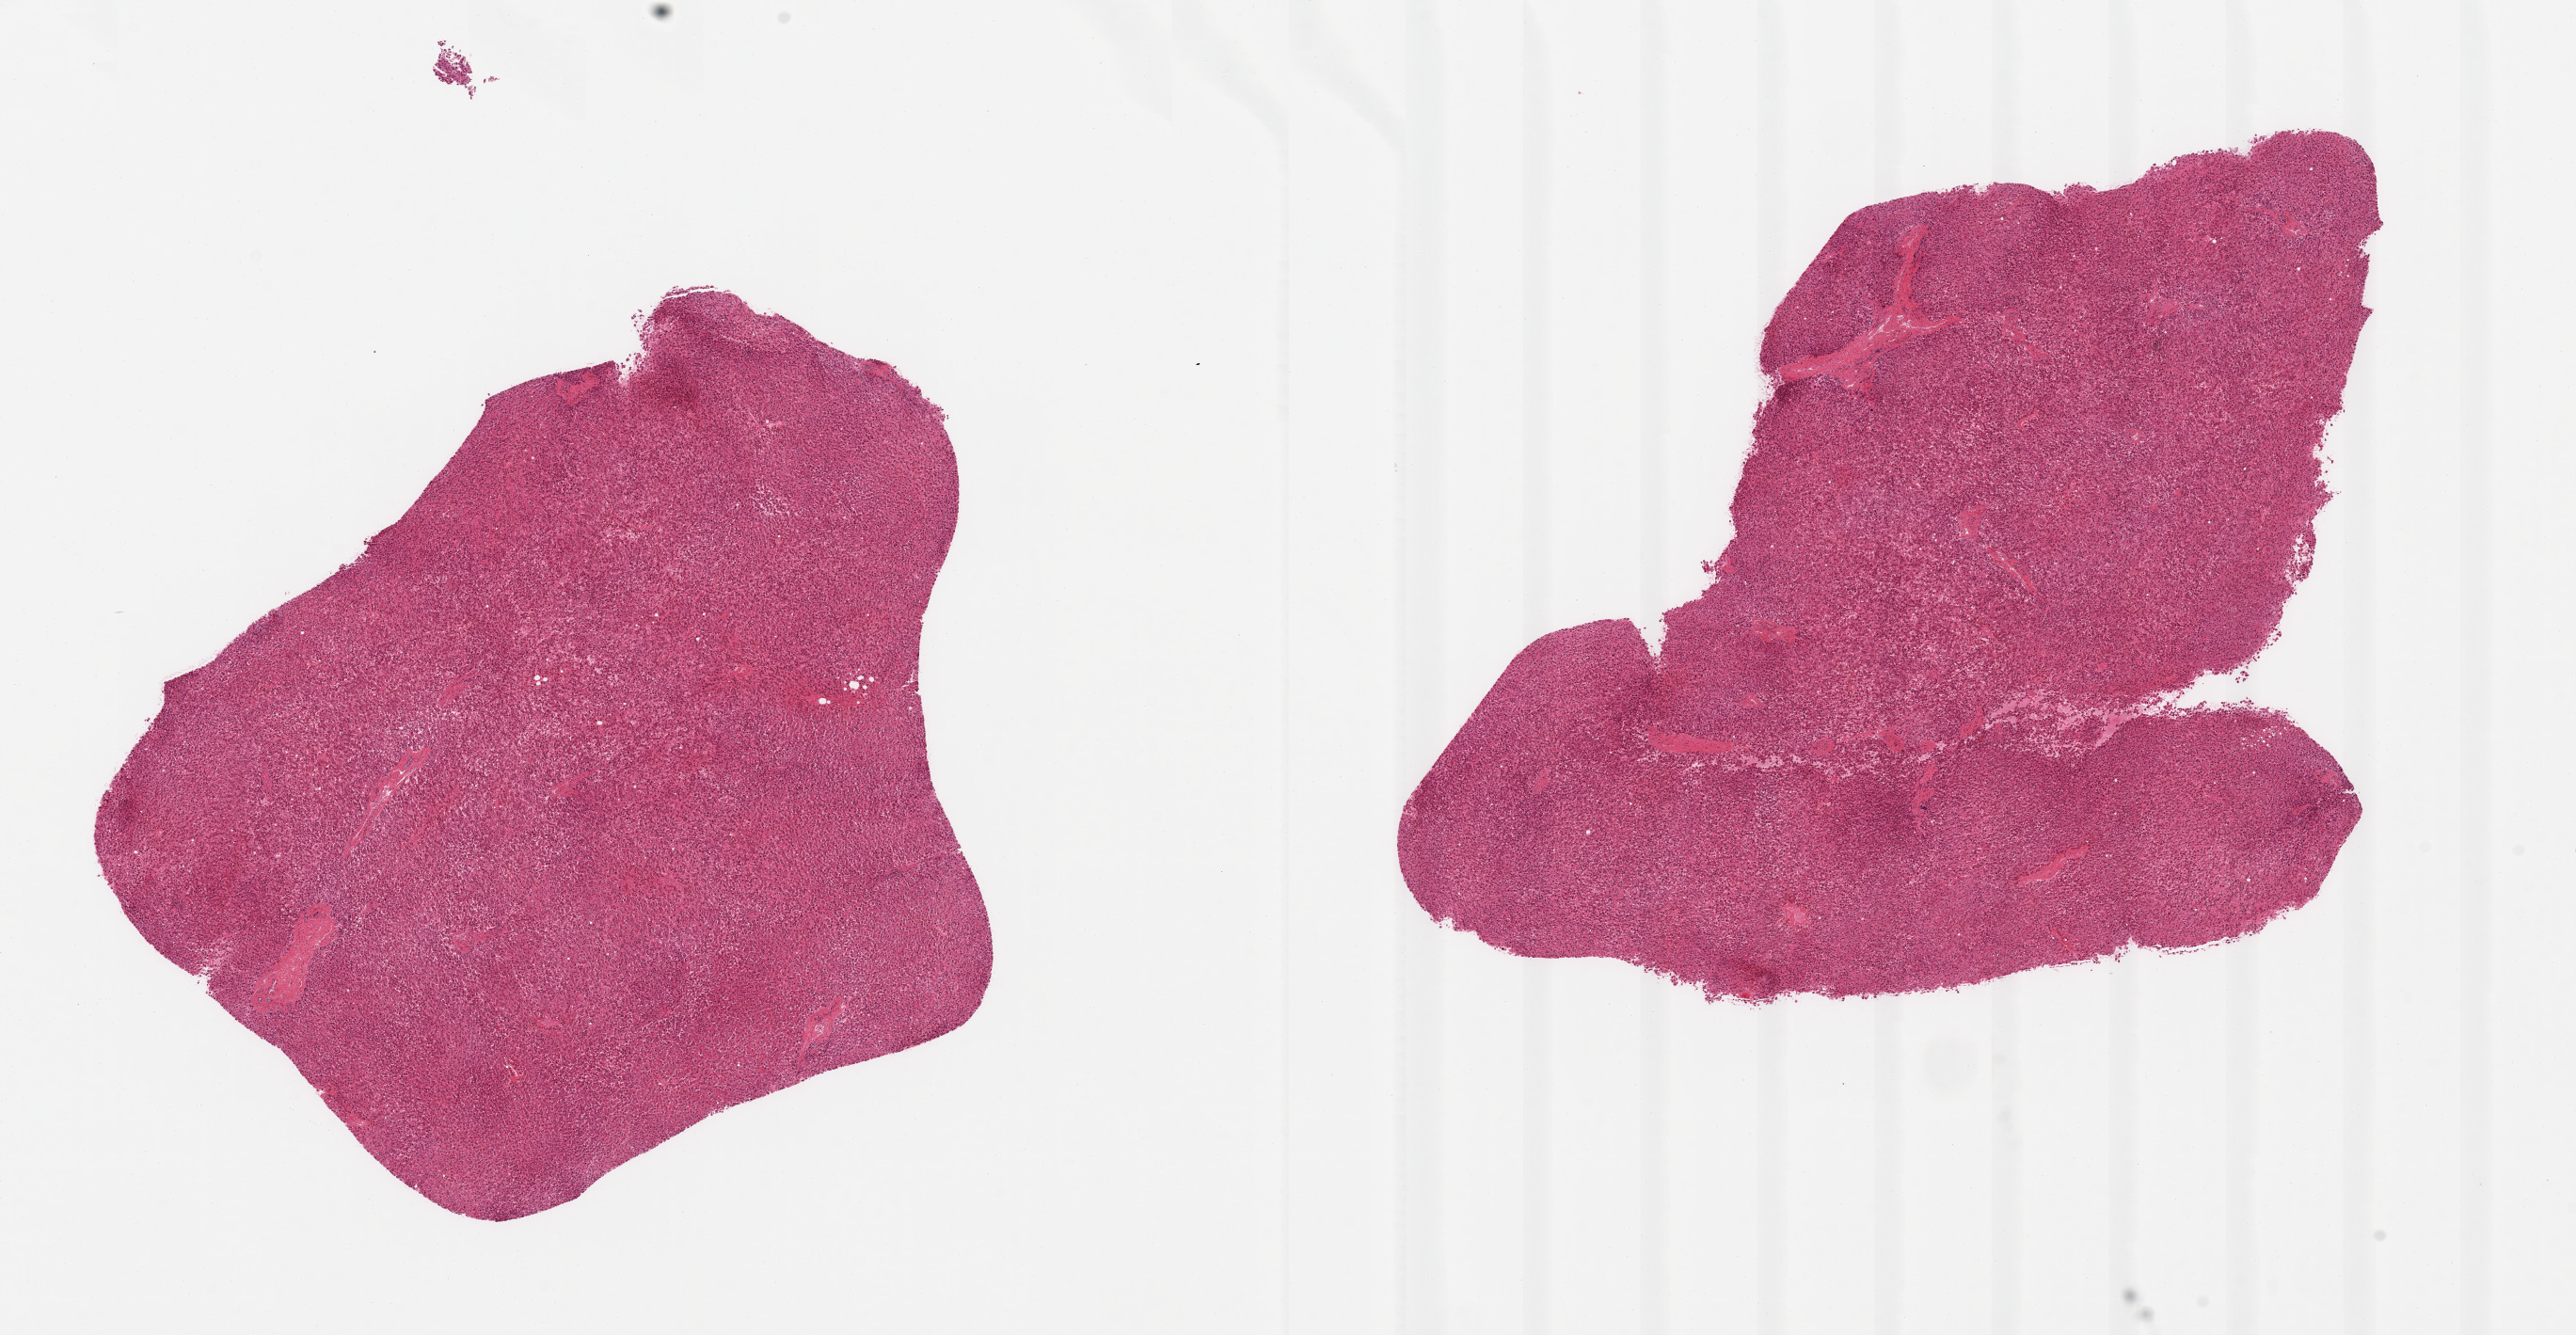
Whole-slide image, hematoxylin and eosin (H&E) stain — low-resolution overview of the scanned area, about 21.7 x 11.2 mm (from a 20x scan). PAXgene-fixed, paraffin-embedded tissue. Target tissue: liver. Donor tissue sample. Donor sex: female.
• reviewer comment on this tissue sample: 2 pieces, moderate passive congestion